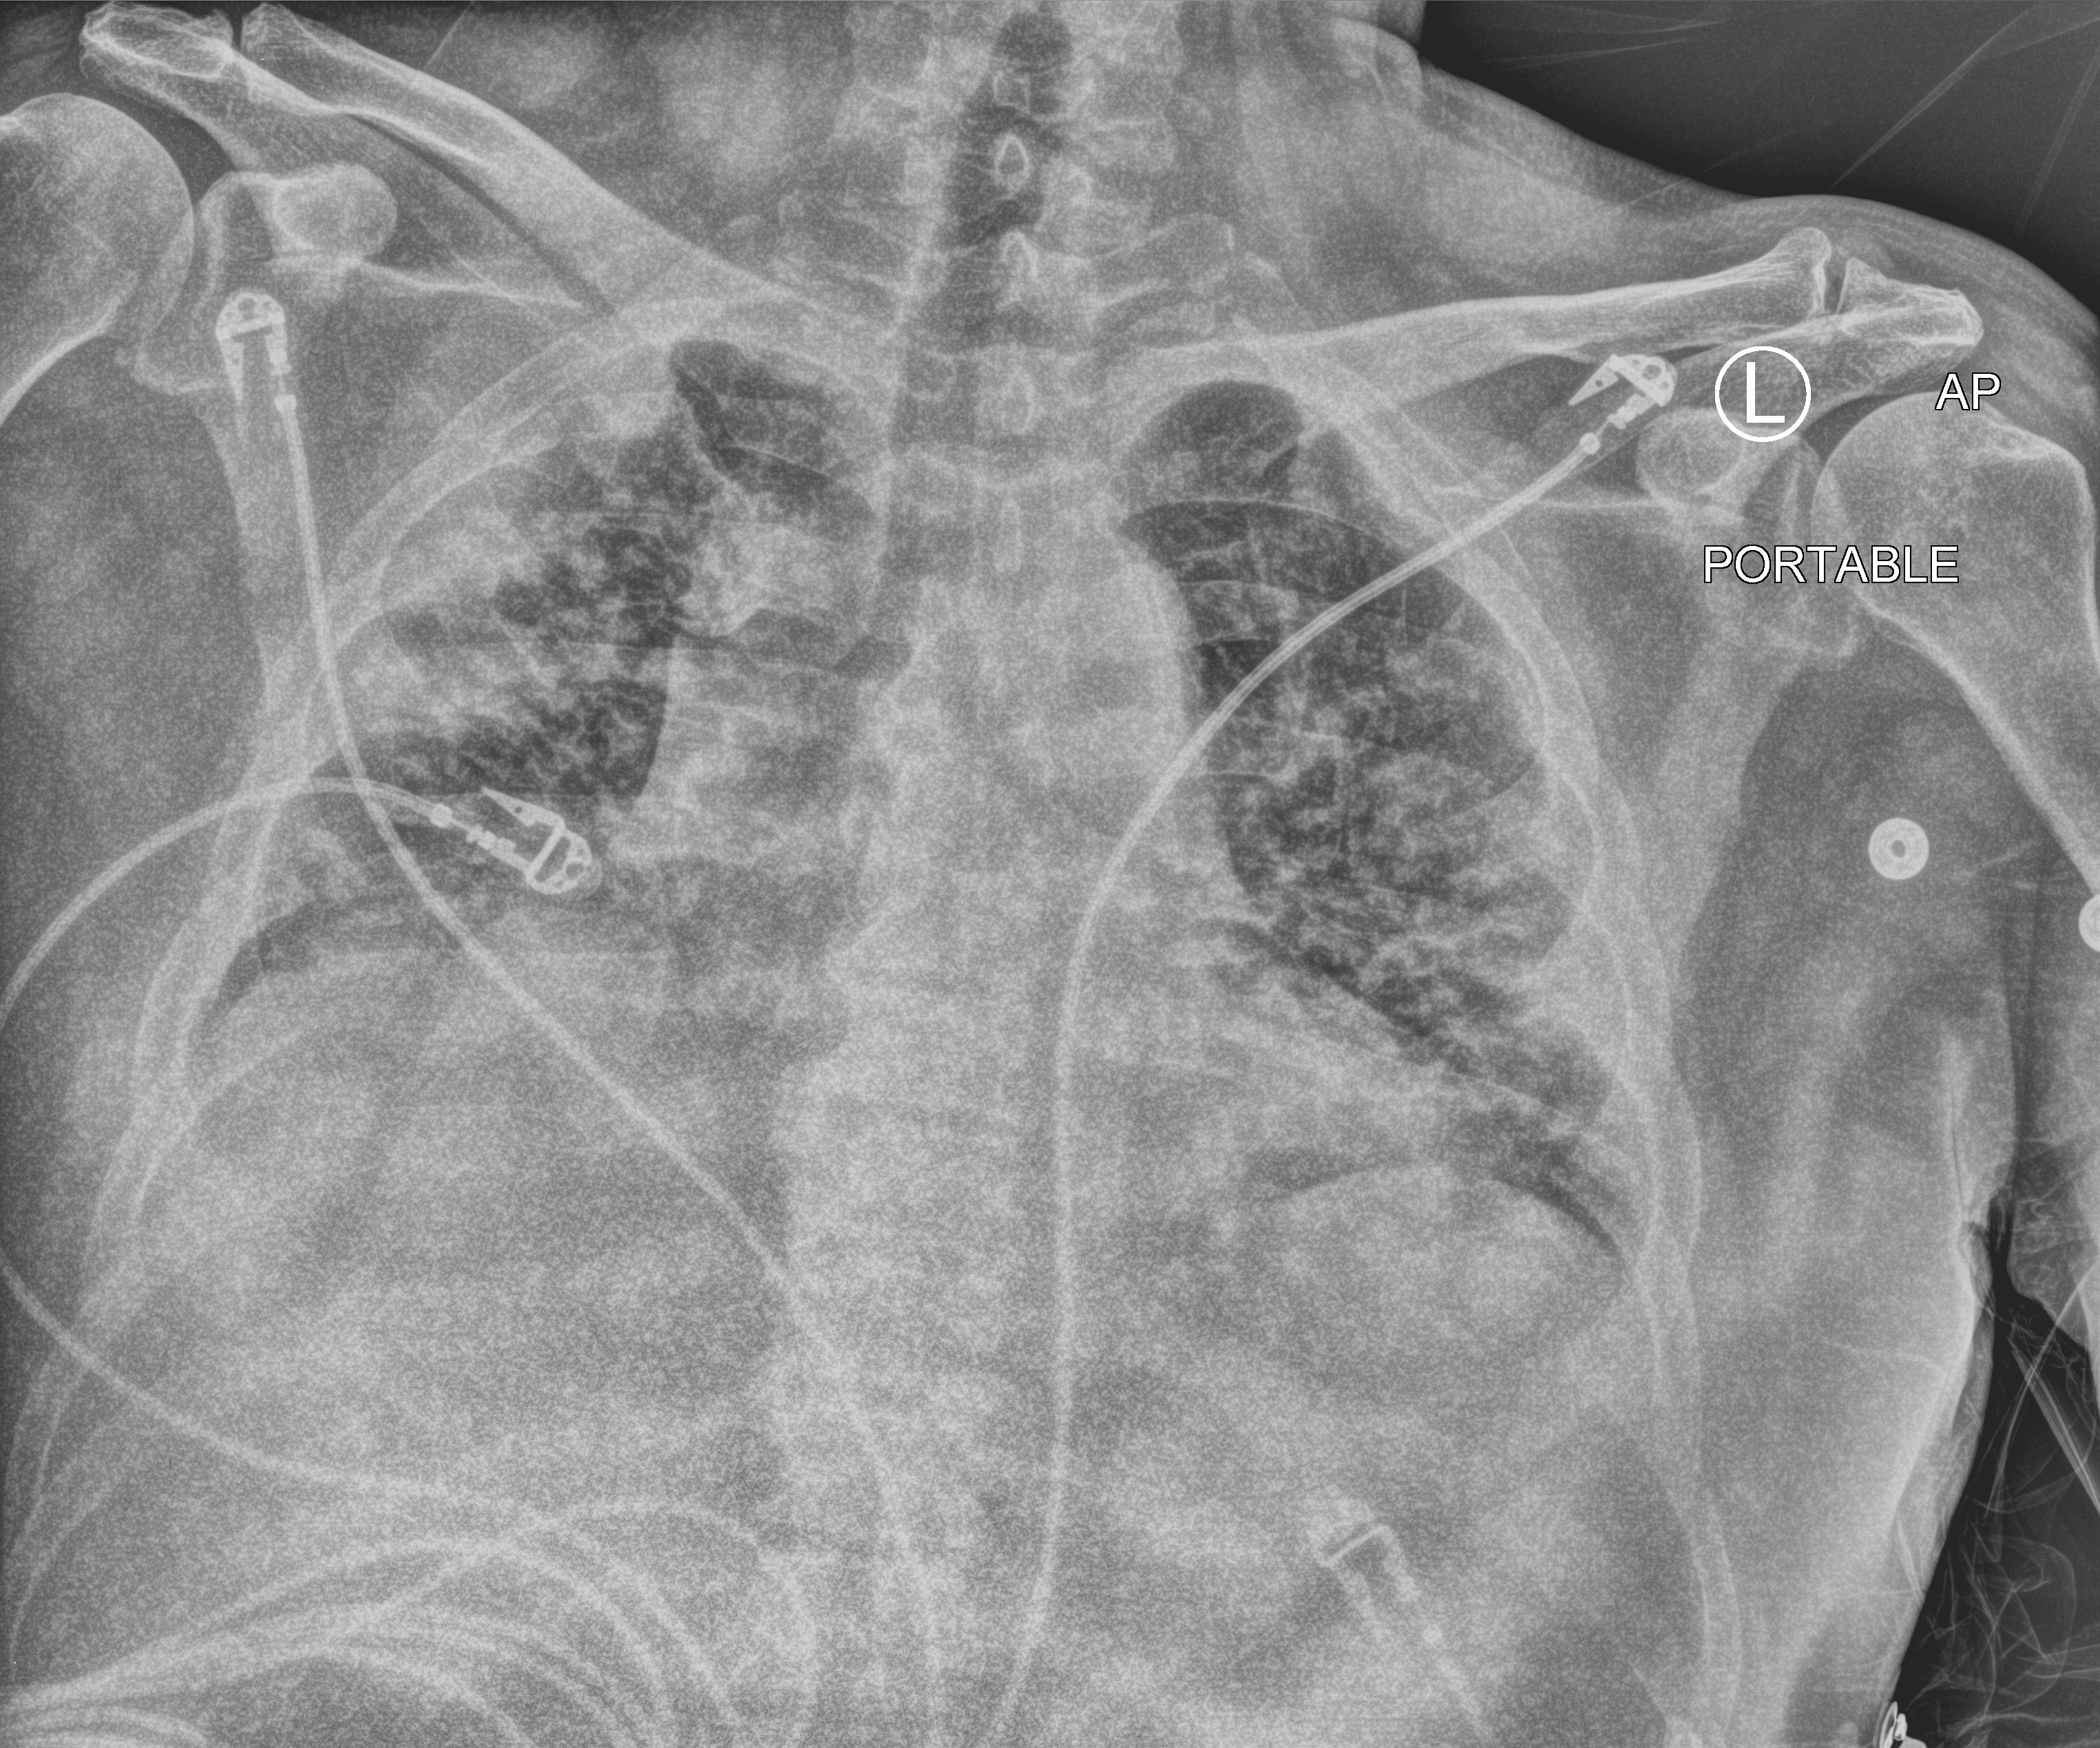
Chest X-ray (portable); anteroposterior (AP) projection. Patient hospitalised with COVID-19; male, aged 60–74 years.
Hospital-stay facts (about this admission, not read from this image; timing relative to this image not recorded): admitted to intensive care during this hospital stay: no.